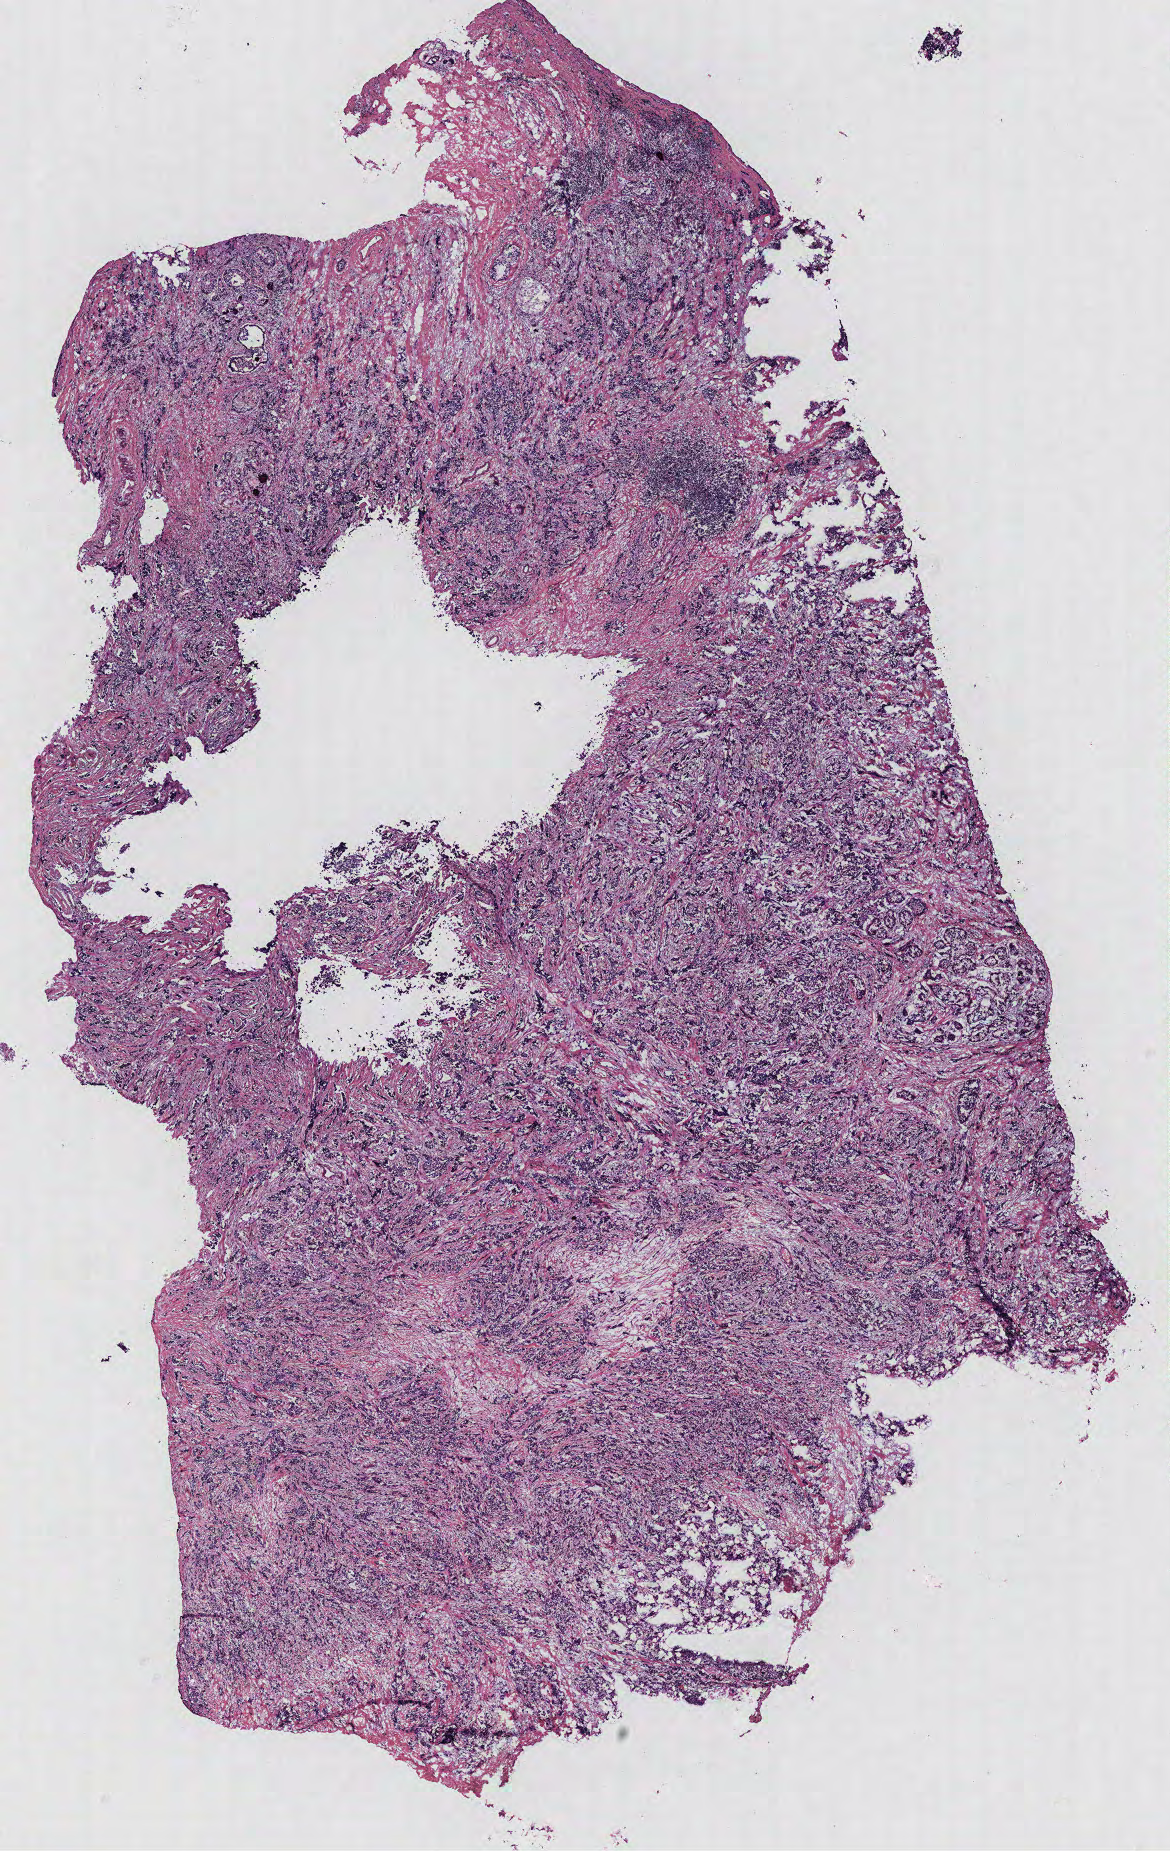
Whole-slide histology image, Hematoxylin and eosin (H&E) stained — a low-resolution overview of the entire scanned area, about 9.4 x 14.8 mm (acquisition: 40x scan); breast, tissue type not recorded. Female, 39 y/o.
• patient diagnosis: Infiltrating duct carcinoma, NOS